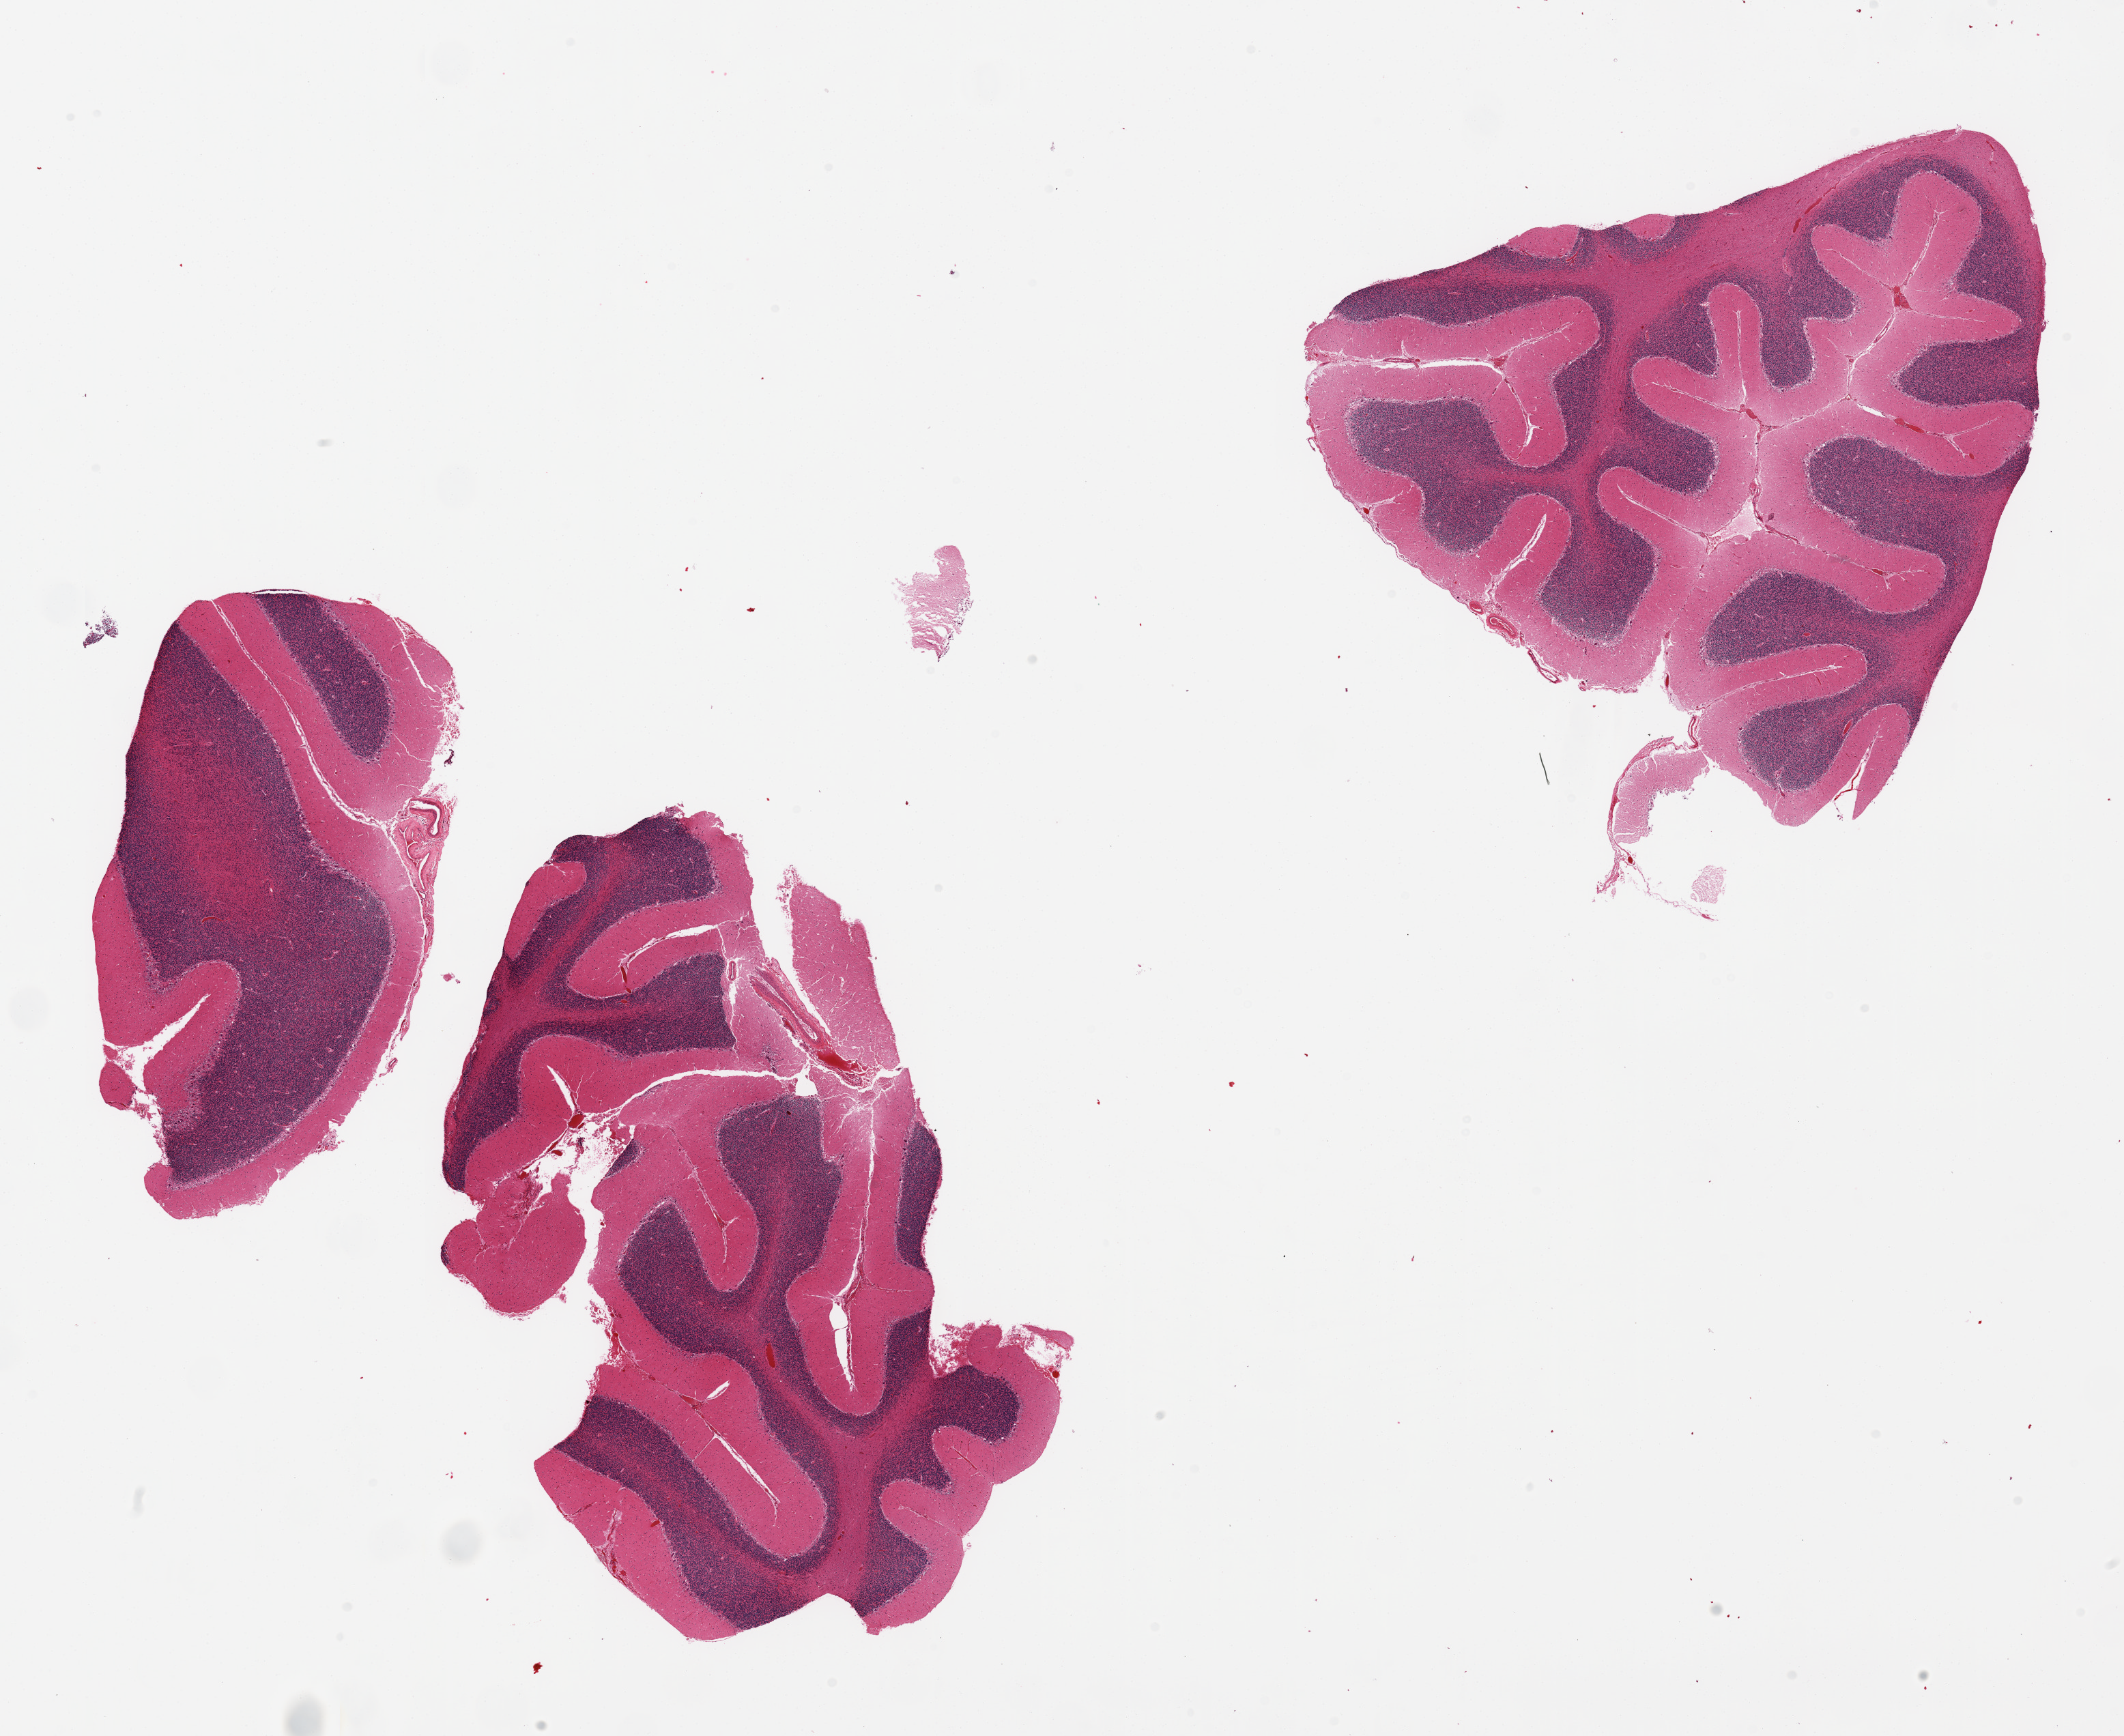
Whole-slide image, hematoxylin and eosin (H&E) stain, brightfield — low-resolution overview of the scanned area, about 24.6 x 20.1 mm (slide scanned at 20x), PAXgene-fixed paraffin-embedded (PFPE) section, section of cerebellum (target tissue), tissue donor sample. Male donor.
• reviewer comment on this tissue sample: 2 pieces, one fragmented, no abnormalities